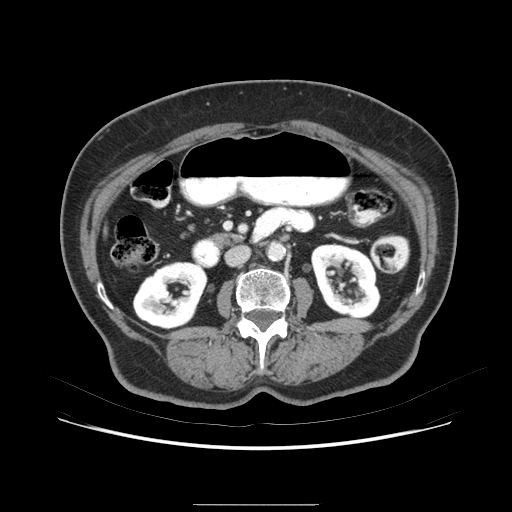
Contrast-enhanced abdominal CT (liver protocol), one axial slice. Position 18 of 79 along the scan axis. Soft-tissue window (W 400 / L 40 HU). 2.5 mm slice thickness. 512 × 512 image matrix. From the clinical record (not read from this slice): diagnosis: hepatocellular carcinoma (patient treated with transarterial chemoembolisation; whether this scan precedes or follows treatment is not stated here); TNM stage (as recorded): Stage-I; Child-Pugh class: A; tumour differentiation: poorly differentiated.
Structures marked on this image (semi-automatically segmented with operator editing):
- liver parenchyma outside the tumour (the mass and vessels are separate outlines, so this box may not span the whole liver): bounding box <100,203,120,258> (left, top, right, bottom; pixels)